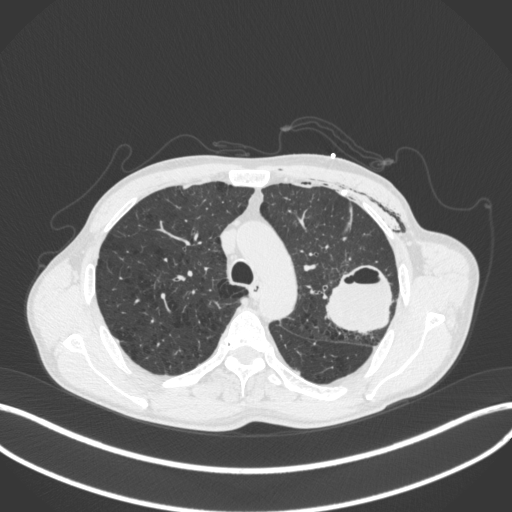
Chest CT, one axial slice. Slice 290 of 416 in the series (ordered by position). 120 kVp. Lung window (W 1500 / L -600 HU). 1 mm slice thickness. 512 × 512 image matrix, field of view 400 × 400 mm. Male patient, age 58 years. Case-level facts recorded for this patient, not image findings: clinical TNM (as recorded): T3 N0 M0.
Annotated regions visible in this slice (bounding box drawn by a radiologist):
- lung tumour (recorded histology: adenocarcinoma): bounding box (x1, y1, x2, y2) in pixels: (324, 264, 396, 335)